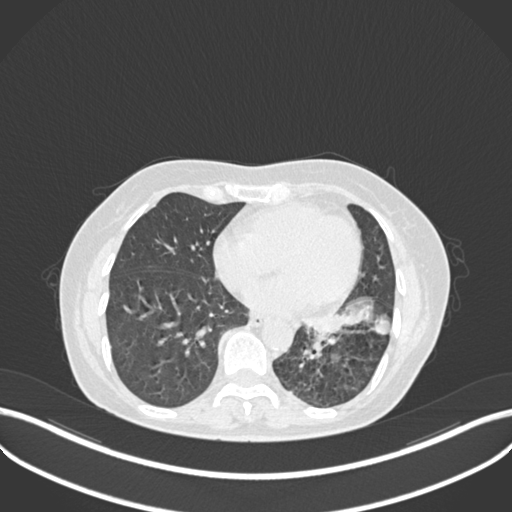
Chest CT, one axial slice. Slice 99 of 270 in the series (ordered by position). Lung window (W 1500 / L -600 HU). 512 × 512 image matrix, field of view 400 × 400 mm. Patient: female, 63 years. Case-level facts recorded for this patient, not image findings: clinical TNM (as recorded): T1b N0 M0; histopathological grade: G2-3.
Outlined on this slice (rectangle marked by the reading radiologist):
- lung tumour (recorded histology: adenocarcinoma): bounding box <300,293,392,341> (left, top, right, bottom; pixels)